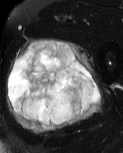
MRI of an extremity soft-tissue mass, one axial slice. Slice 31 of 60 in the series (ordered by position). T2-weighted fat-saturated. MR volume resampled by the dataset authors to the PET/CT grid (not the native acquisition matrix). 123 × 153 image matrix, field of view 120 × 149 mm. Male patient. Case-level facts recorded for this patient, not image findings: histological type: pleiomorphic liposarcoma; grade: high; site of the primary tumour: left thigh.
Outlined on this slice (expert contour drawn on MRI and transferred to this co-registered scan by the dataset authors):
- gross tumour volume including surrounding oedema: bounding box <6,38,103,135> (left, top, right, bottom; pixels)
- gross tumour volume (mass): <8,40,101,126>